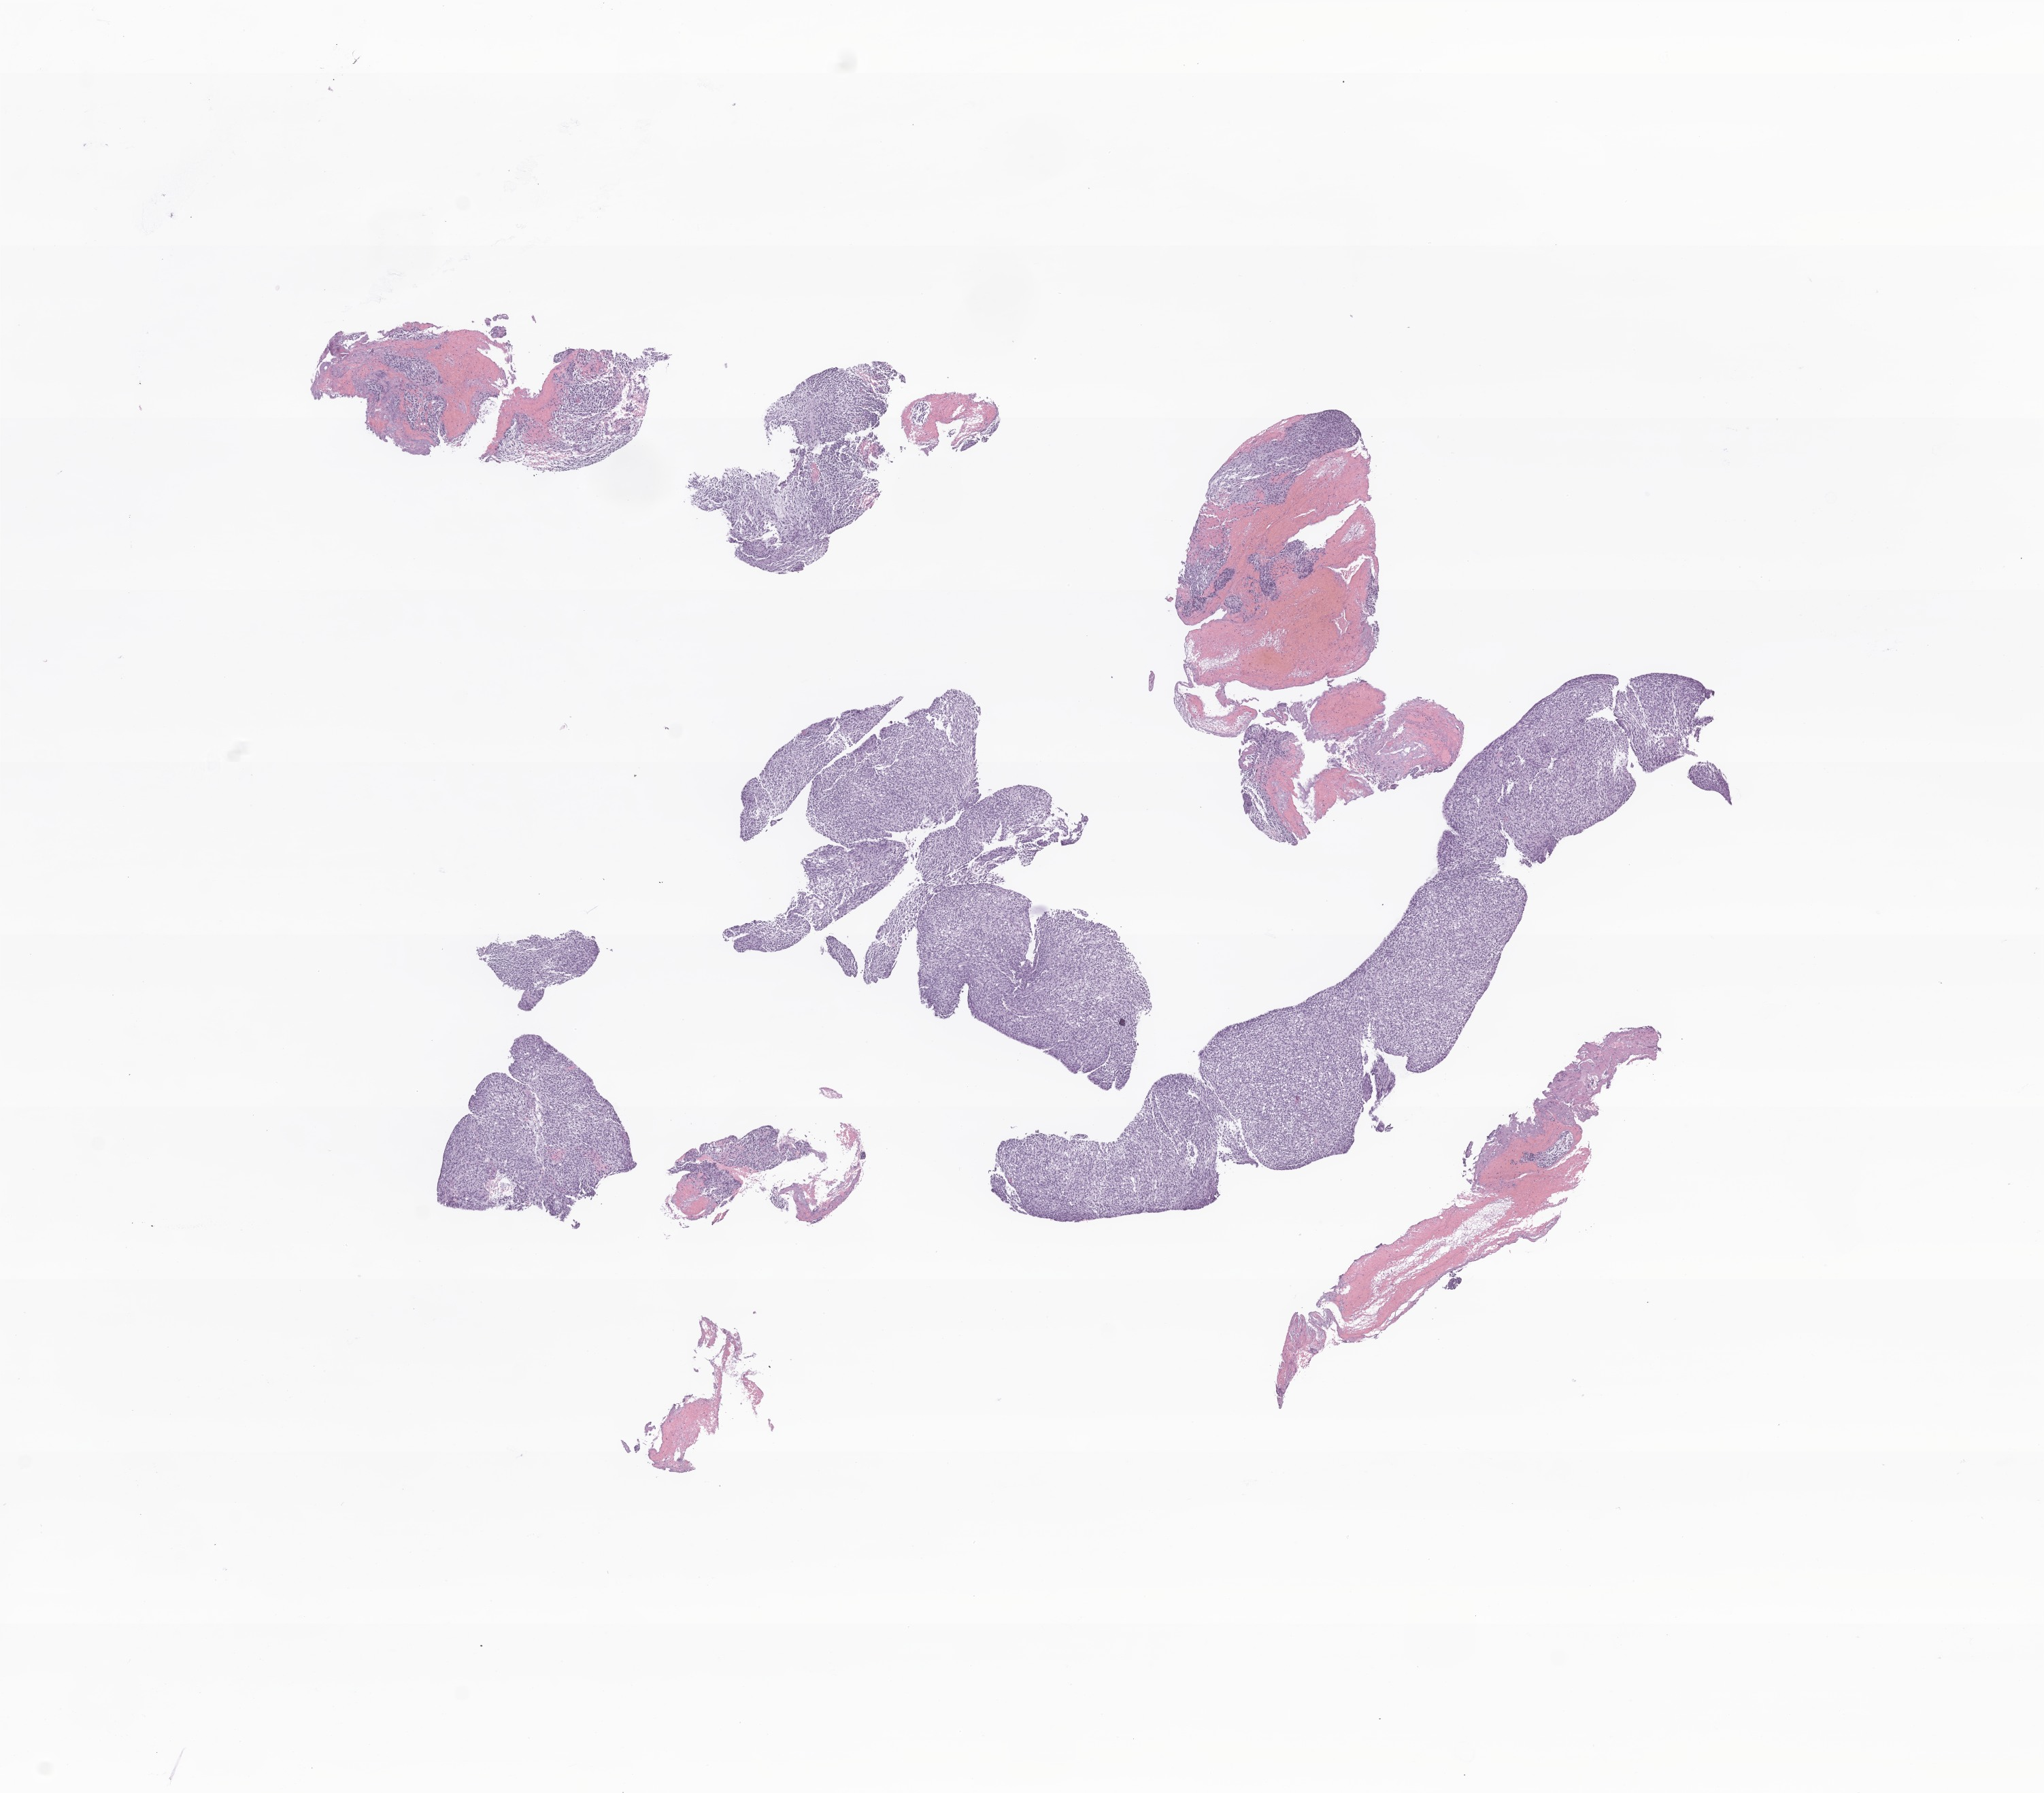
Whole-slide image, hematoxylin and eosin (H&E) stain of tumor tissue from the lung — shown as a low-resolution overview of the whole scanned area (about 12.7 x 11.1 mm). Formalin-fixed, paraffin-embedded (FFPE) tissue. Patient: female, age 990 days (about 2.7 years).
Diagnosis (ICD-O-3 morphology term): Pleuropulmonary blastoma.